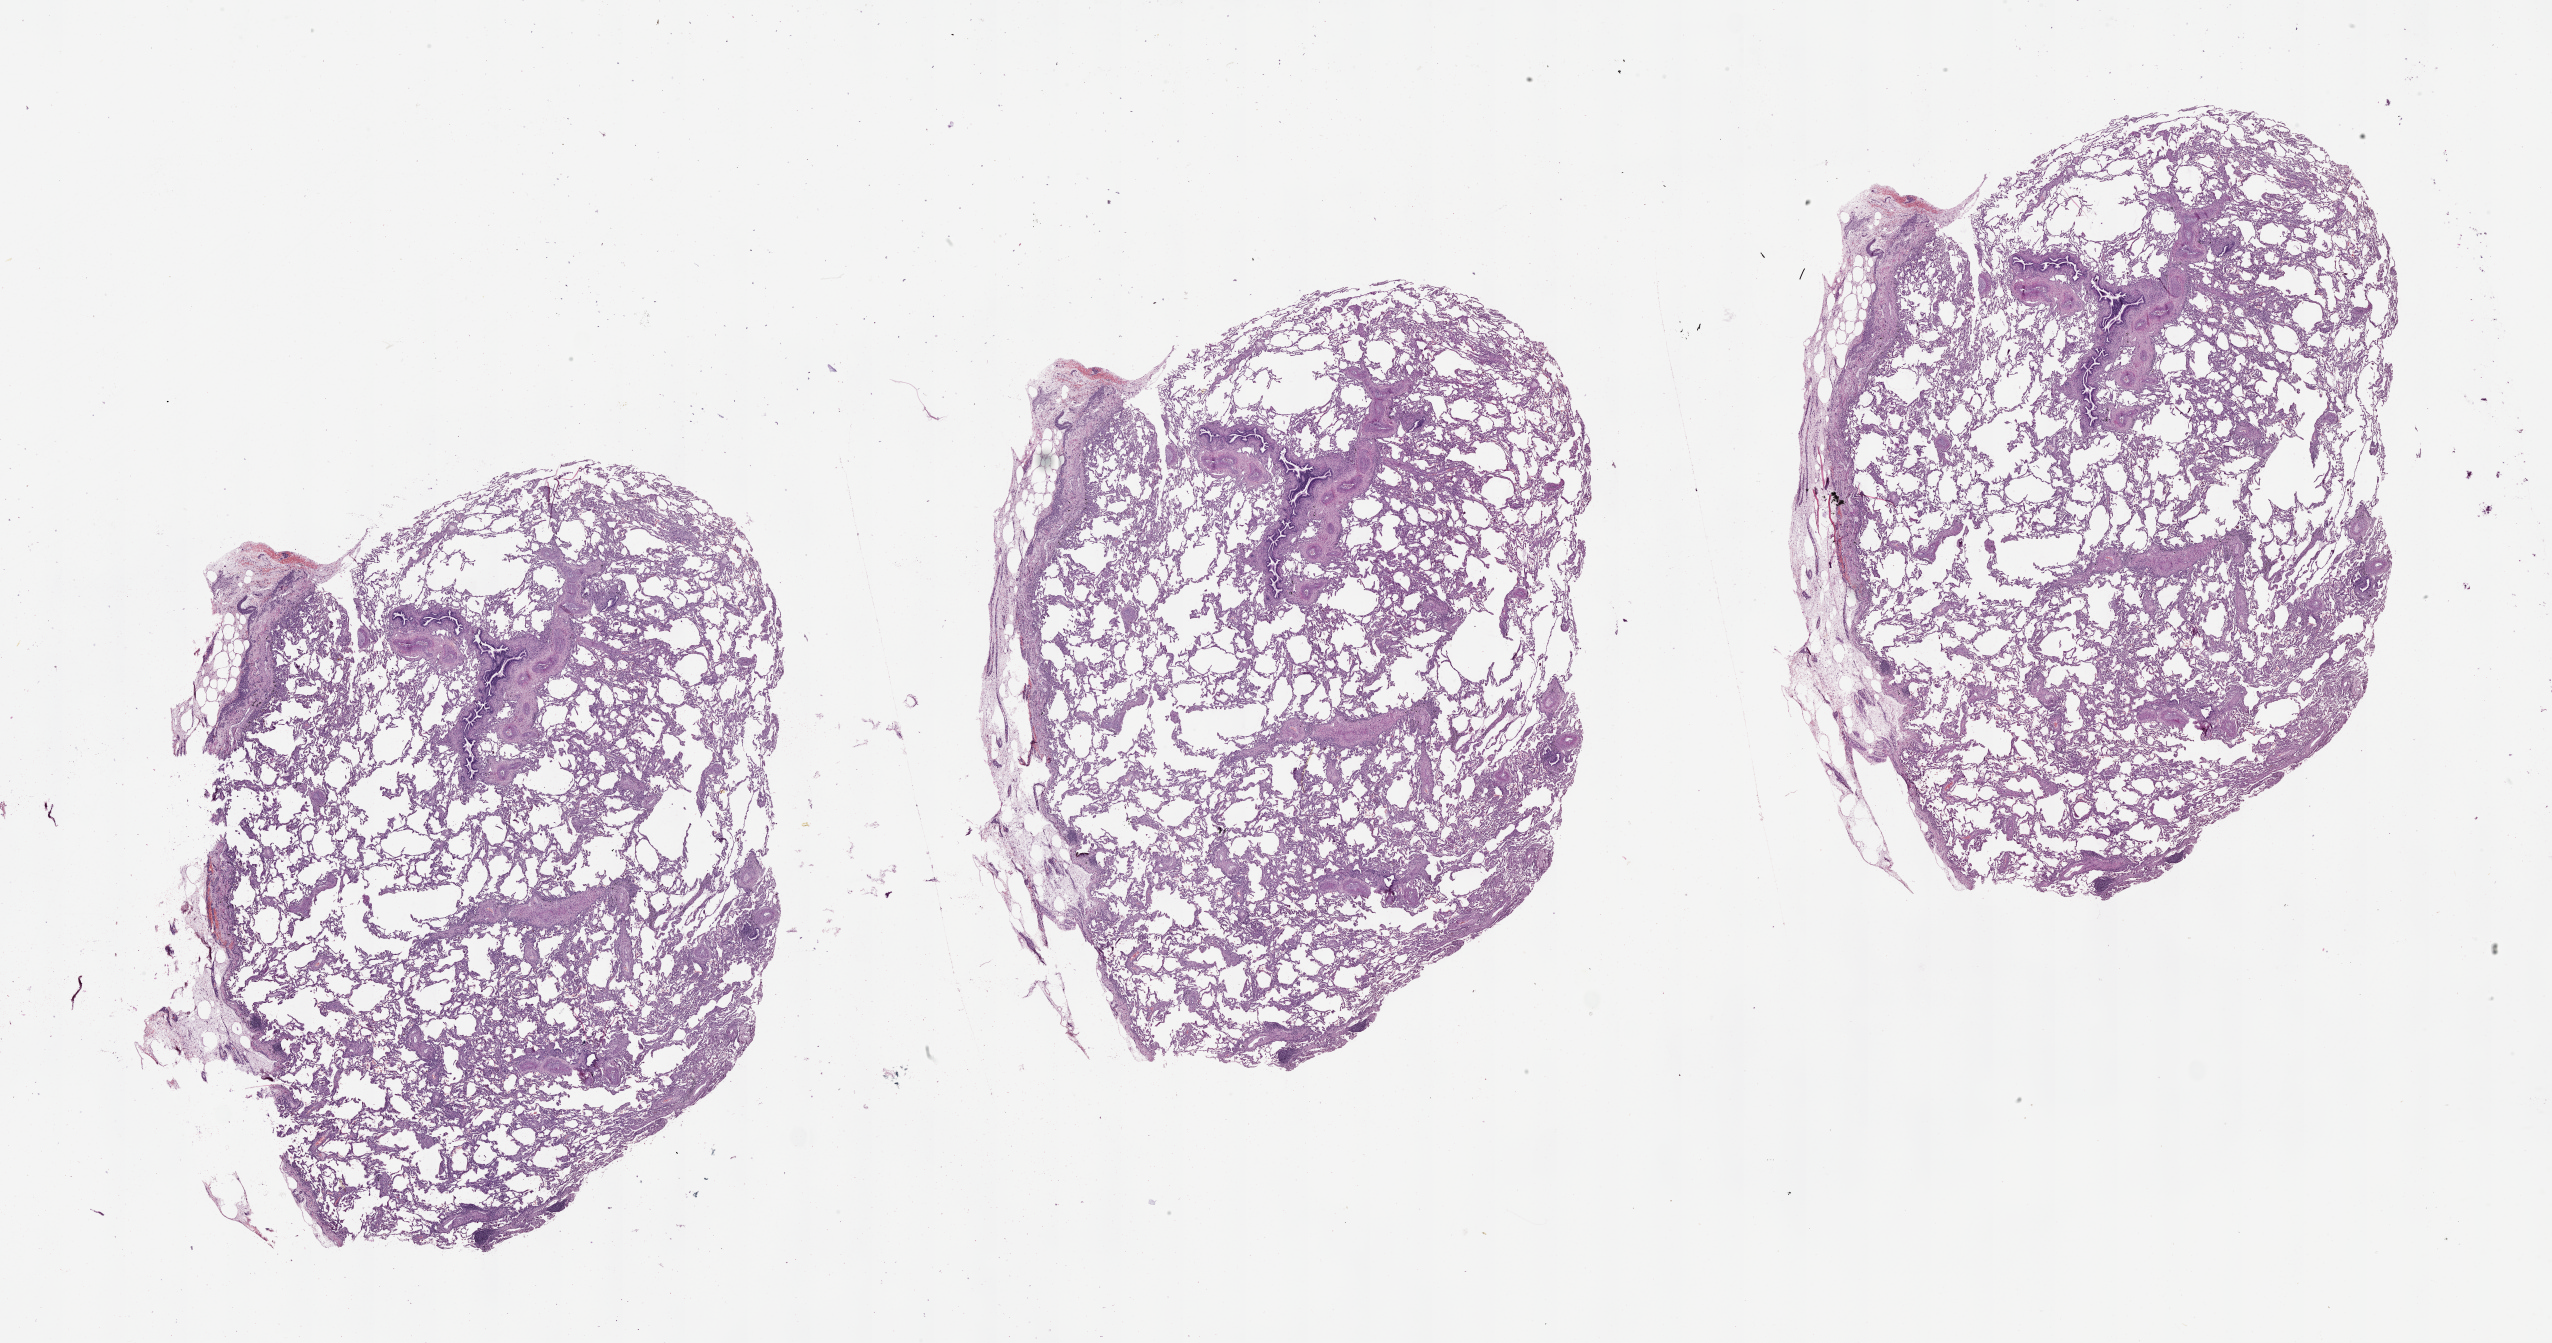
Digitized Hematoxylin and eosin (H&E) stained tissue section (whole slide) — low-resolution overview of the scanned area, about 41.1 x 21.6 mm (from a 20x scan). Normal (non-tumour) tissue sample, lung. Male, 72 y/o.
This section: normal (non-tumour) tissue from the same patient. Patient diagnosis (cohort enrolment): squamous cell carcinoma (lung).